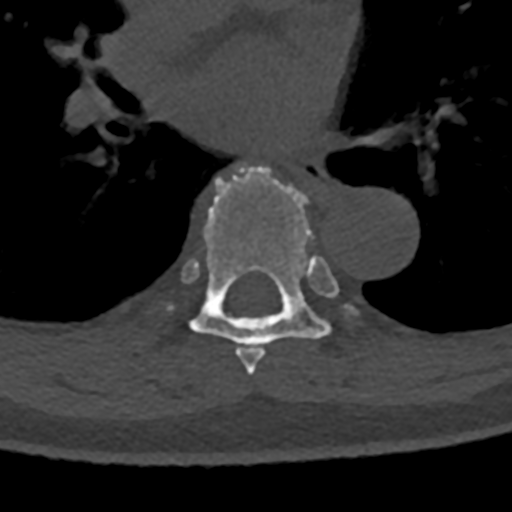
CT including the spine, one axial slice. Slice 767 of 797 in the series (ordered by position). Reconstruction kernel Br40s/3. 120 kVp. Bone window (W 1800 / L 400 HU). 512 × 512 image matrix, field of view 160 × 160 mm. Patient: male, 74 years. From the clinical record (not read from this slice): primary cancer: renal; vertebrae with lytic lesions (as recorded): T10, L1, L2, L3, L4, L5.
Structures marked on this image (semi-automatic segmentation, software-assisted and operator-edited):
- T6 vertebra: bounding box [x1, y1, x2, y2] px = [238, 347, 265, 375]
- T7 vertebra: [156, 166, 355, 367]